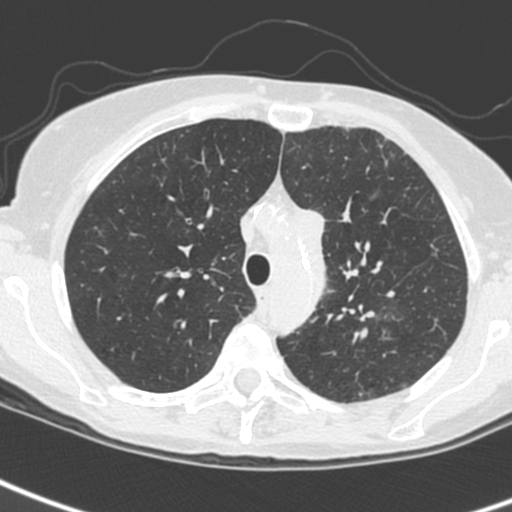
Low-dose screening chest CT, one axial slice; position 187 of 242 along the scan axis; 120 kVp; lung window (W 1500 / L -600 HU); 1.3 mm slice thickness; 512 × 512 image matrix, field of view 284 × 284 mm.
Annotated regions visible in this slice (manually delineated by an expert):
- lesion 3 (tumor, upper lobe of left lung): bounding box <299,209,327,299> (left, top, right, bottom; pixels)